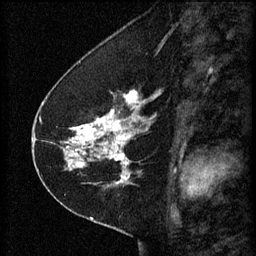
Breast MRI (dynamic contrast-enhanced), one sagittal slice. Slice 26 of 60 in the series (ordered by position). 3 images stored at this slice position (order not interpretable as contrast timing). 1.5 T. TE 4.2 ms, TR 8.2 ms. 256 × 256 image matrix, field of view 180 × 180 mm. Patient: female, 41 years.
Annotated regions visible in this slice (semi-automatic segmentation, software-assisted and operator-edited):
- analysis volume of interest (the breast-tissue region the enhancement analysis was run in; not a lesion): bounding box (x1, y1, x2, y2) in pixels: (67, 92, 156, 173)
- tumour enhancement mask (voxels above the 70 % enhancement threshold inside the analysis volume of interest): (67, 94, 151, 173)